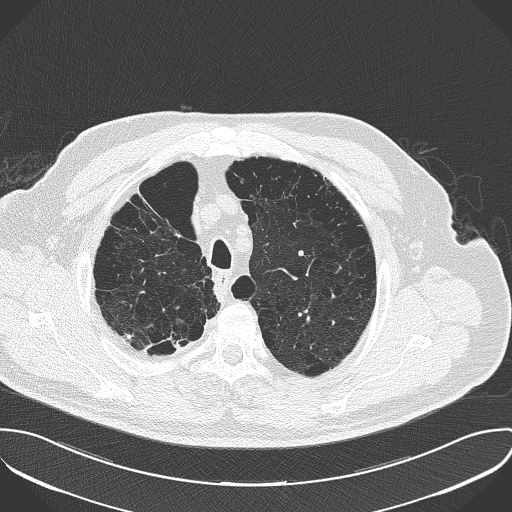
Low-dose screening chest CT, axial slice. First (baseline) screen. Lung window (W 1500 / L -600 HU). 2 mm slice thickness. Lung (sharp) reconstruction kernel (B50f). Male, age 68 years at enrolment. Current smoker at enrolment.
• Expert reader's lesion annotation, box from (x=123, y=322) to (x=197, y=365) px.
• The screening reader recorded 3 non-calcified nodules or masses ≥4 mm on this exam (left lower lobe, left upper lobe, right lower lobe); which of them this box marks is not recorded.
• Participant outcome: lung cancer diagnosed 661 days after this screen (after the second annual screen) — adenocarcinoma, NOS, right upper lobe, stage IV (AJCC 6th edition), 29 mm at pathology.